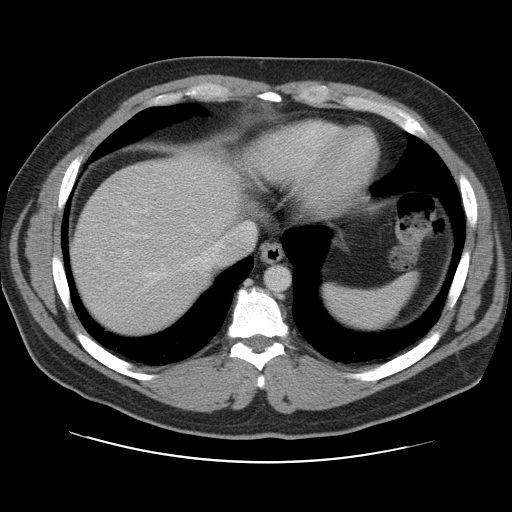
Contrast-enhanced abdominal CT, one axial slice. Slice 95 of 109 in the series (ordered by position). 120 kVp. Intravenous contrast given. Soft-tissue window (W 400 / L 40 HU). 5 mm slice thickness. 512 × 512 image matrix, field of view 402 × 402 mm. Male patient, age 35 years. Case-level facts recorded for this patient, not image findings: diagnosis: colorectal cancer liver metastases, imaged before liver resection.
Annotated regions visible in this slice (expert manual segmentation):
- hepatic veins: bounding box <144,223,254,281> (left, top, right, bottom; pixels)
- liver: <71,155,241,335>
- planned liver remnant (the part of the liver to remain after resection): <71,155,241,335>